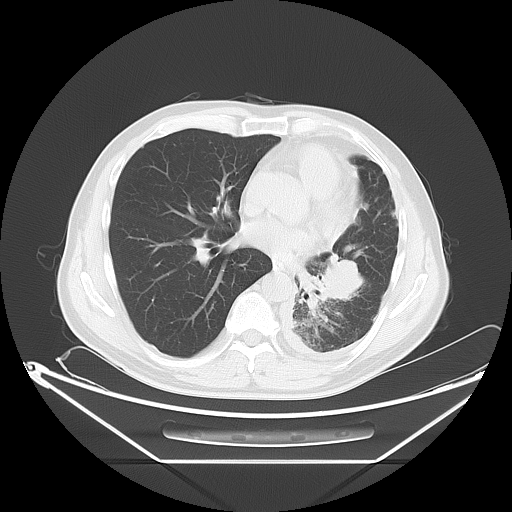
Chest CT, one axial slice; slice 30 of 63 in the series (ordered by position); reconstruction kernel LUNG; 120 kVp; lung window (W 1500 / L -600 HU); 5 mm slice thickness; 512 × 512 image matrix, field of view 442 × 442 mm. Patient: male, 60 years. Case-level facts recorded for this patient, not image findings: clinical TNM (as recorded): T4 N1 M1.
Outlined on this slice (rectangle marked by the reading radiologist):
- lung tumour (recorded histology: adenocarcinoma): bounding box (x1, y1, x2, y2) in pixels: (298, 238, 363, 310)